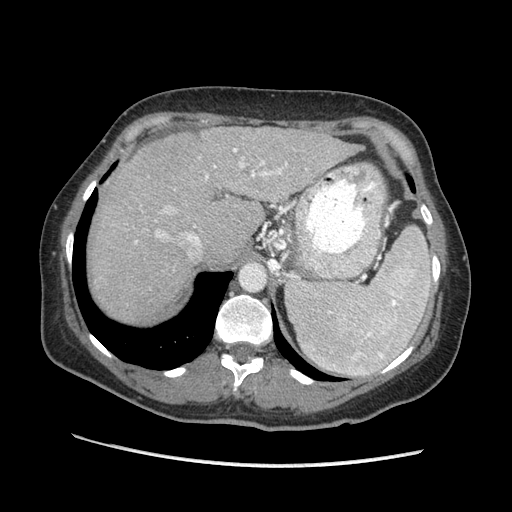
Contrast-enhanced abdominal CT (liver protocol), one axial slice. Slice 143 of 170 in the series (ordered by position). Soft-tissue window (W 400 / L 40 HU). 2.5 mm slice thickness. 512 × 512 image matrix. Case-level facts recorded for this patient, not image findings: diagnosis: hepatocellular carcinoma (patient treated with transarterial chemoembolisation; whether this scan precedes or follows treatment is not stated here); TNM stage (as recorded): Stage-II; Child-Pugh class: A; tumour size: 4 cm.
Annotated regions visible in this slice (semi-automatically segmented with operator editing):
- abdominal aorta: bounding box [x1, y1, x2, y2] px = [240, 264, 265, 290]
- liver parenchyma outside the tumour (the mass and vessels are separate outlines, so this box may not span the whole liver): [90, 126, 356, 322]
- liver vessels: [135, 148, 288, 255]